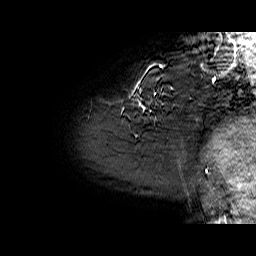
Breast MRI (dynamic contrast-enhanced), one sagittal slice; slice 55 of 60 in the series (ordered by position); dynamic contrast-enhanced series, time point 2 of 6 at this slice position (early post-contrast); 1.5 T; TE 6.4 ms, TR 32.9 ms; 4 mm slice thickness; 256 × 256 image matrix, field of view 200 × 200 mm. Female patient. From the clinical record (not read from this slice): setting: breast cancer imaged before/during neoadjuvant chemotherapy; receptor status: HER2-positive.
Structures marked on this image (semi-automatic segmentation, software-assisted and operator-edited):
- analysis volume of interest (the breast-tissue region the enhancement analysis was run in; not a lesion): bounding box (x1, y1, x2, y2) in pixels: (130, 62, 210, 128)
- tumour enhancement mask (voxels above the 100 % enhancement threshold inside the analysis volume of interest): (149, 64, 162, 67)